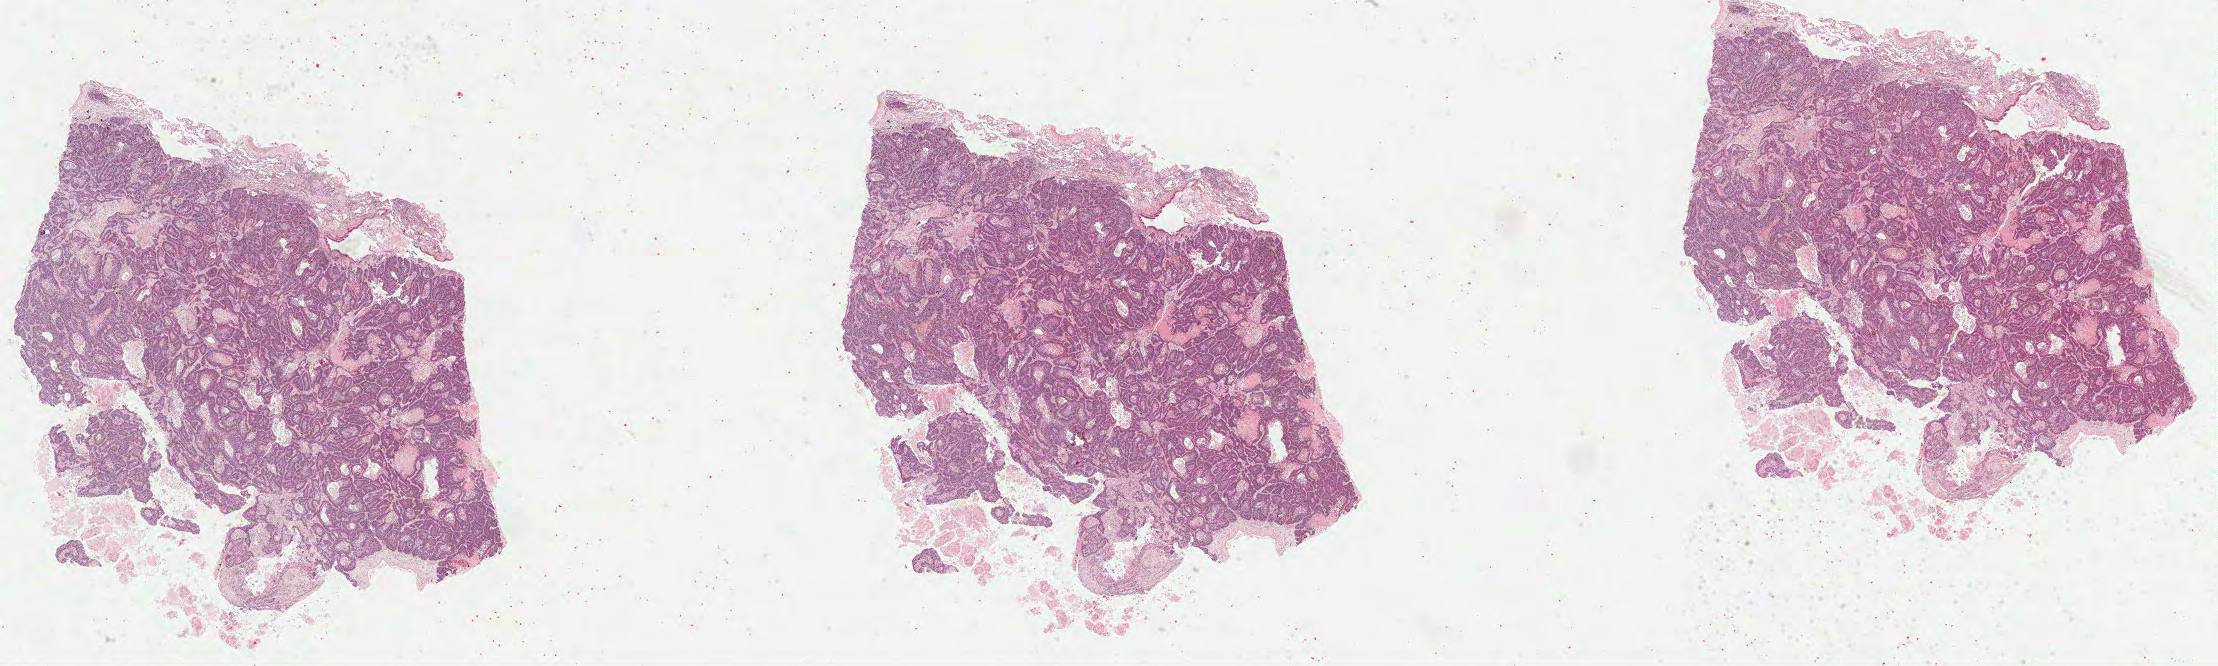
H&E-stained whole-slide image, whole scanned area (about 35.8 x 10.7 mm, acquisition: 40x scan) shown as a low-resolution overview; formalin-fixed paraffin-embedded (FFPE) diagnostic section; lung, primary tumour sample. Male, age 81 years at initial diagnosis.
AJCC pathologic stage: IIB. Pathologic diagnosis: Squamous cell carcinoma, NOS (lower lobe, lung).